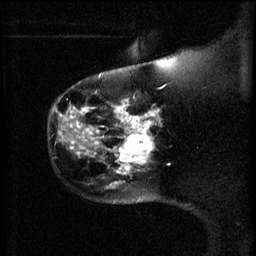
Breast MRI (dynamic contrast-enhanced), one sagittal slice. Position 49 of 60 along the scan axis. 3 images stored at this slice position (order not interpretable as contrast timing). 1.5 T. TE 4.2 ms, TR 11 ms. 2 mm slice thickness. 256 × 256 image matrix, field of view 180 × 180 mm. Patient: female, 44 years.
Annotated regions visible in this slice (semi-automatically segmented with operator editing):
- analysis volume of interest (the breast-tissue region the enhancement analysis was run in; not a lesion): bounding box <116,124,155,175> (left, top, right, bottom; pixels)
- tumour enhancement mask (voxels above the 70 % enhancement threshold inside the analysis volume of interest): <116,124,155,175>